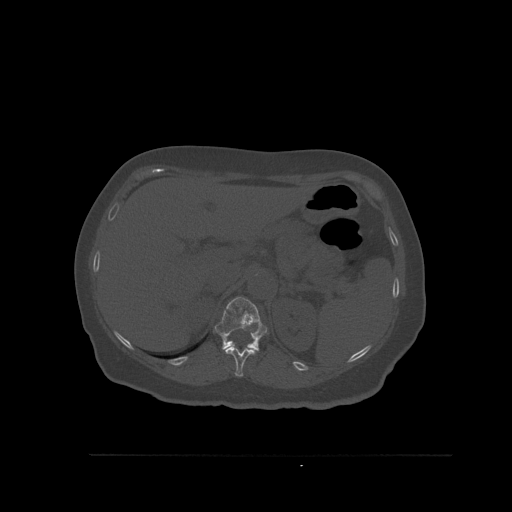
CT including the spine, one axial slice; position 293 of 527 along the scan axis; bone window (W 1800 / L 400 HU); 1.5 mm slice thickness; 512 × 512 image matrix, field of view 470 × 470 mm. Patient: female, 73 years. Case-level facts recorded for this patient, not image findings: primary cancer: breast; vertebrae with lytic lesions (as recorded): L2.
Annotated regions visible in this slice (semi-automatically segmented with operator editing):
- T11 vertebra: bounding box [x1, y1, x2, y2] px = [223, 346, 255, 377]
- T12 vertebra: [214, 297, 268, 355]